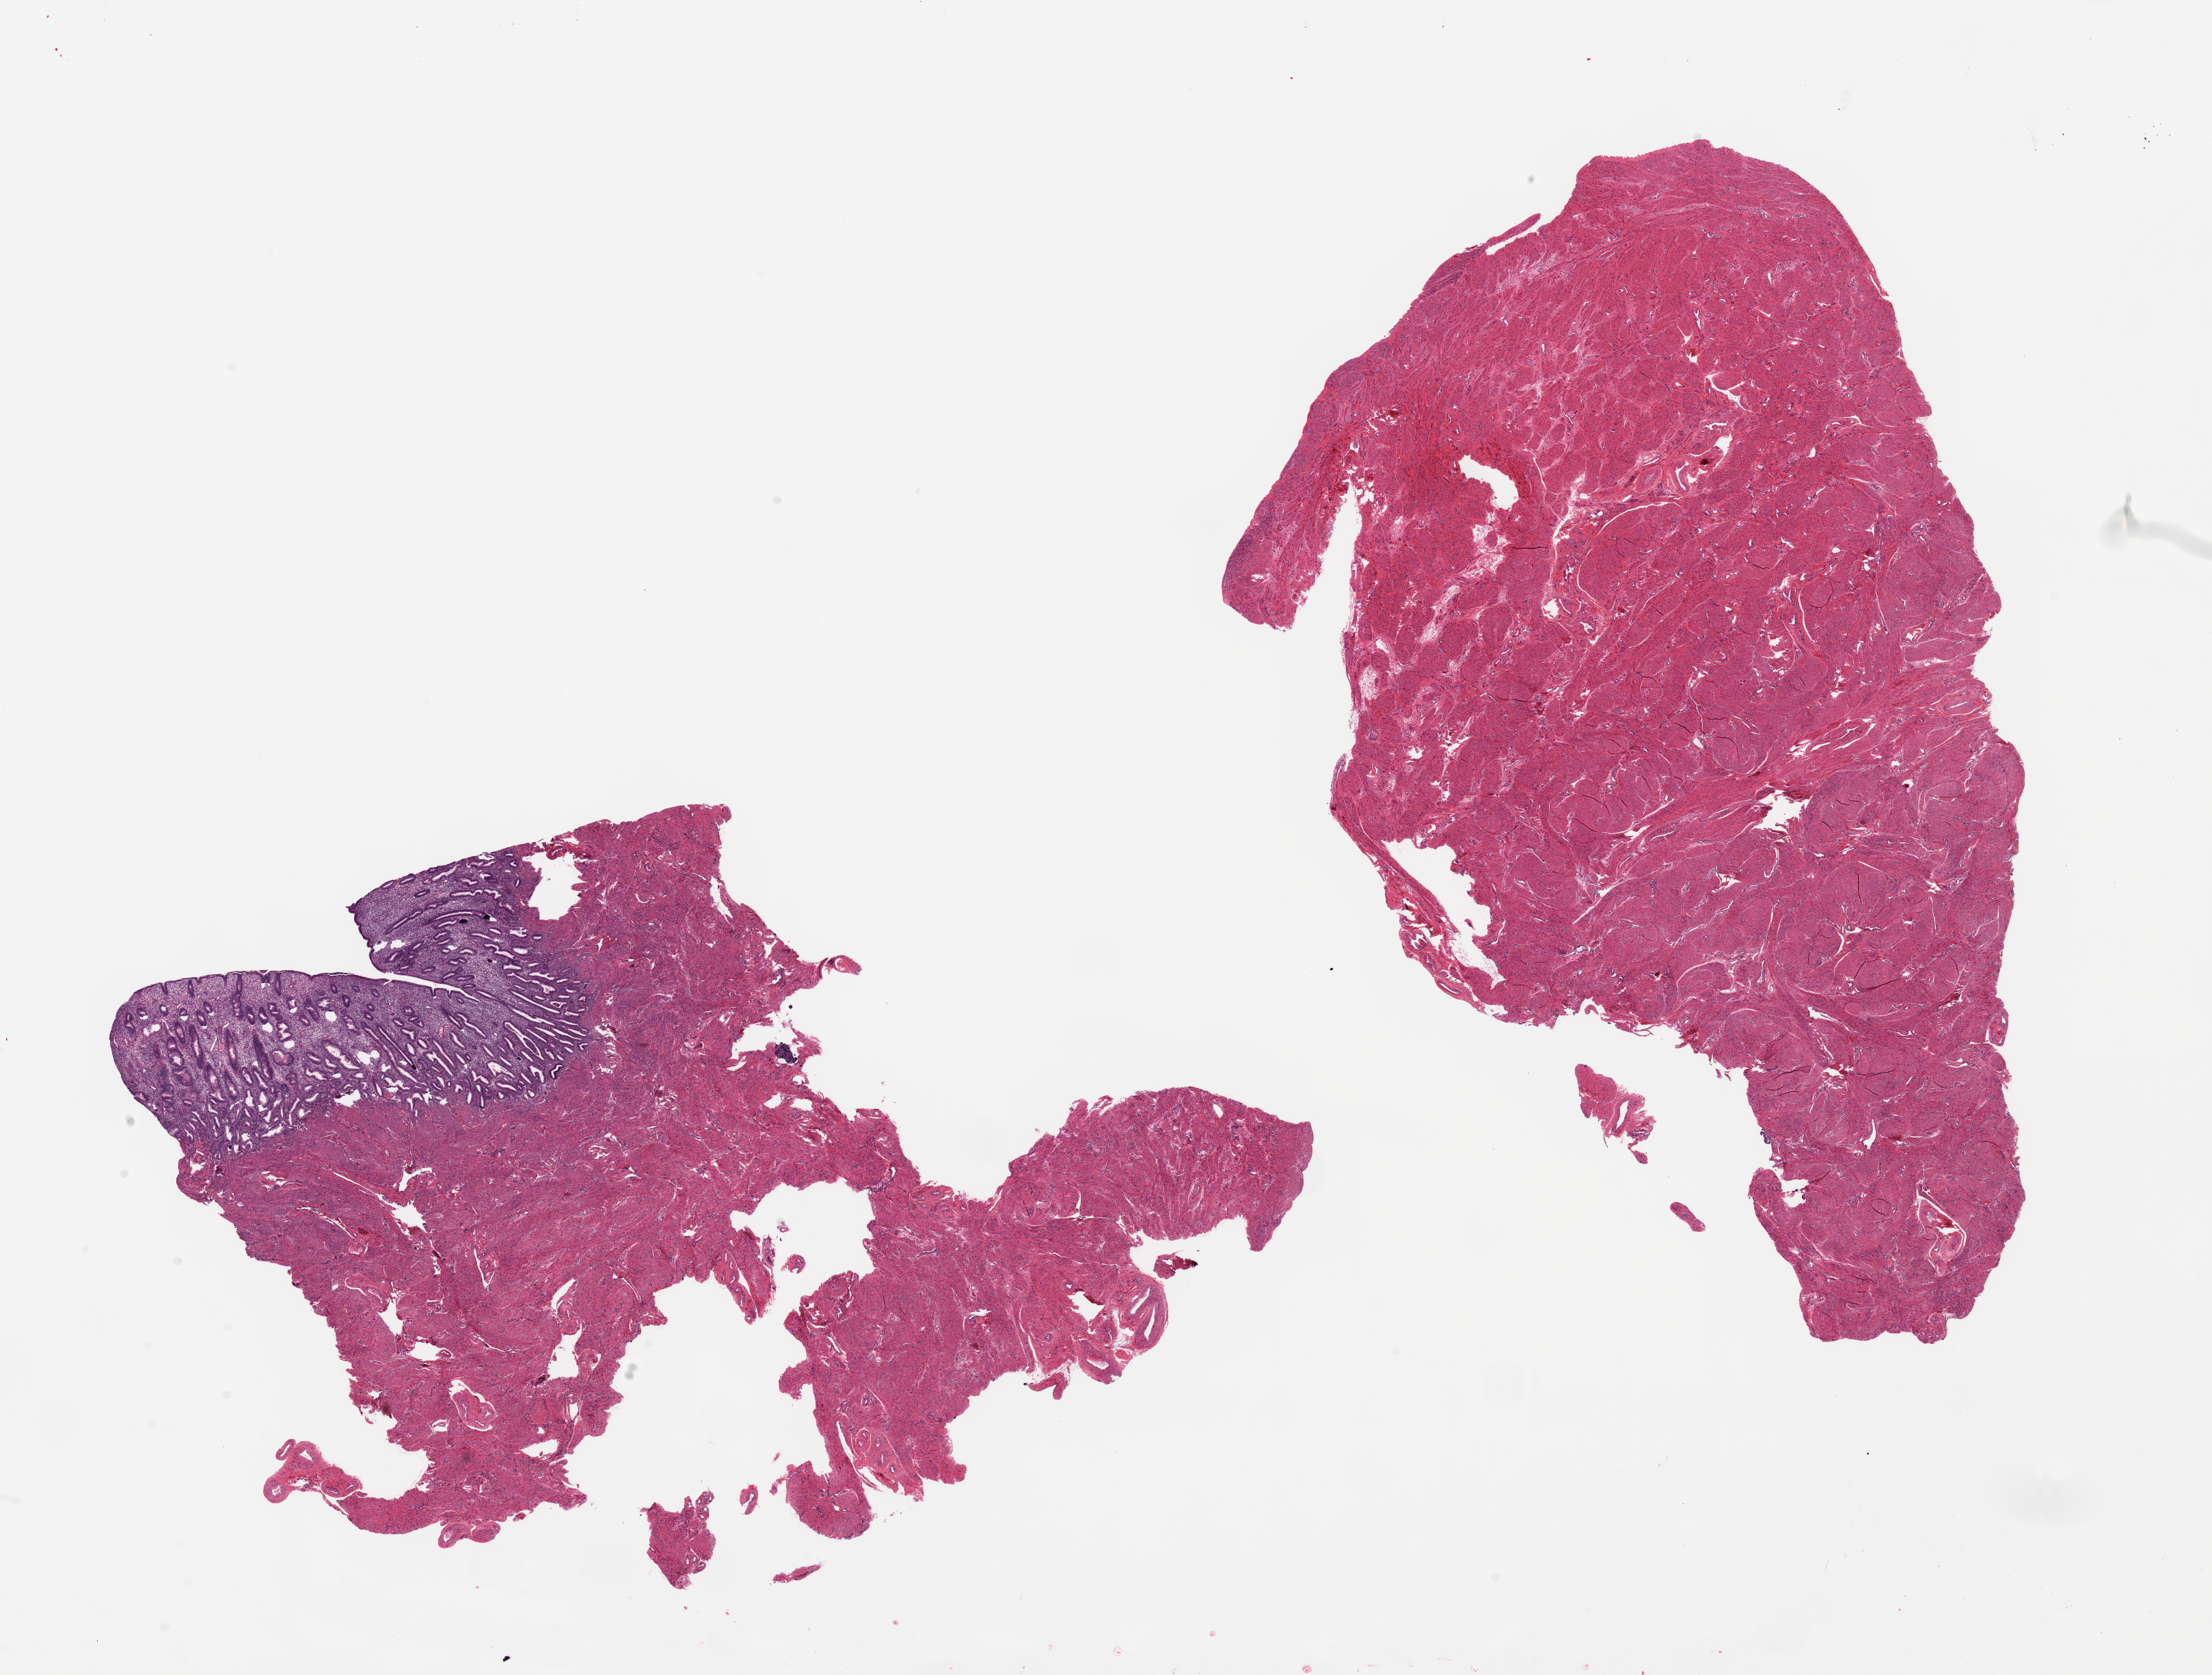
H&E whole-slide image, whole scanned area (about 25.6 x 19.4 mm, acquisition: 20x scan) shown as a low-resolution overview; PAXgene-fixed, paraffin-embedded tissue; sampled site (target tissue): uterus; tissue donor sample.
Reviewer comment on this tissue sample: 2 pieces, 1, 6x6 mm with secretory endometrium 2mm thick; 1, 14x7.7 mm without endometrium.